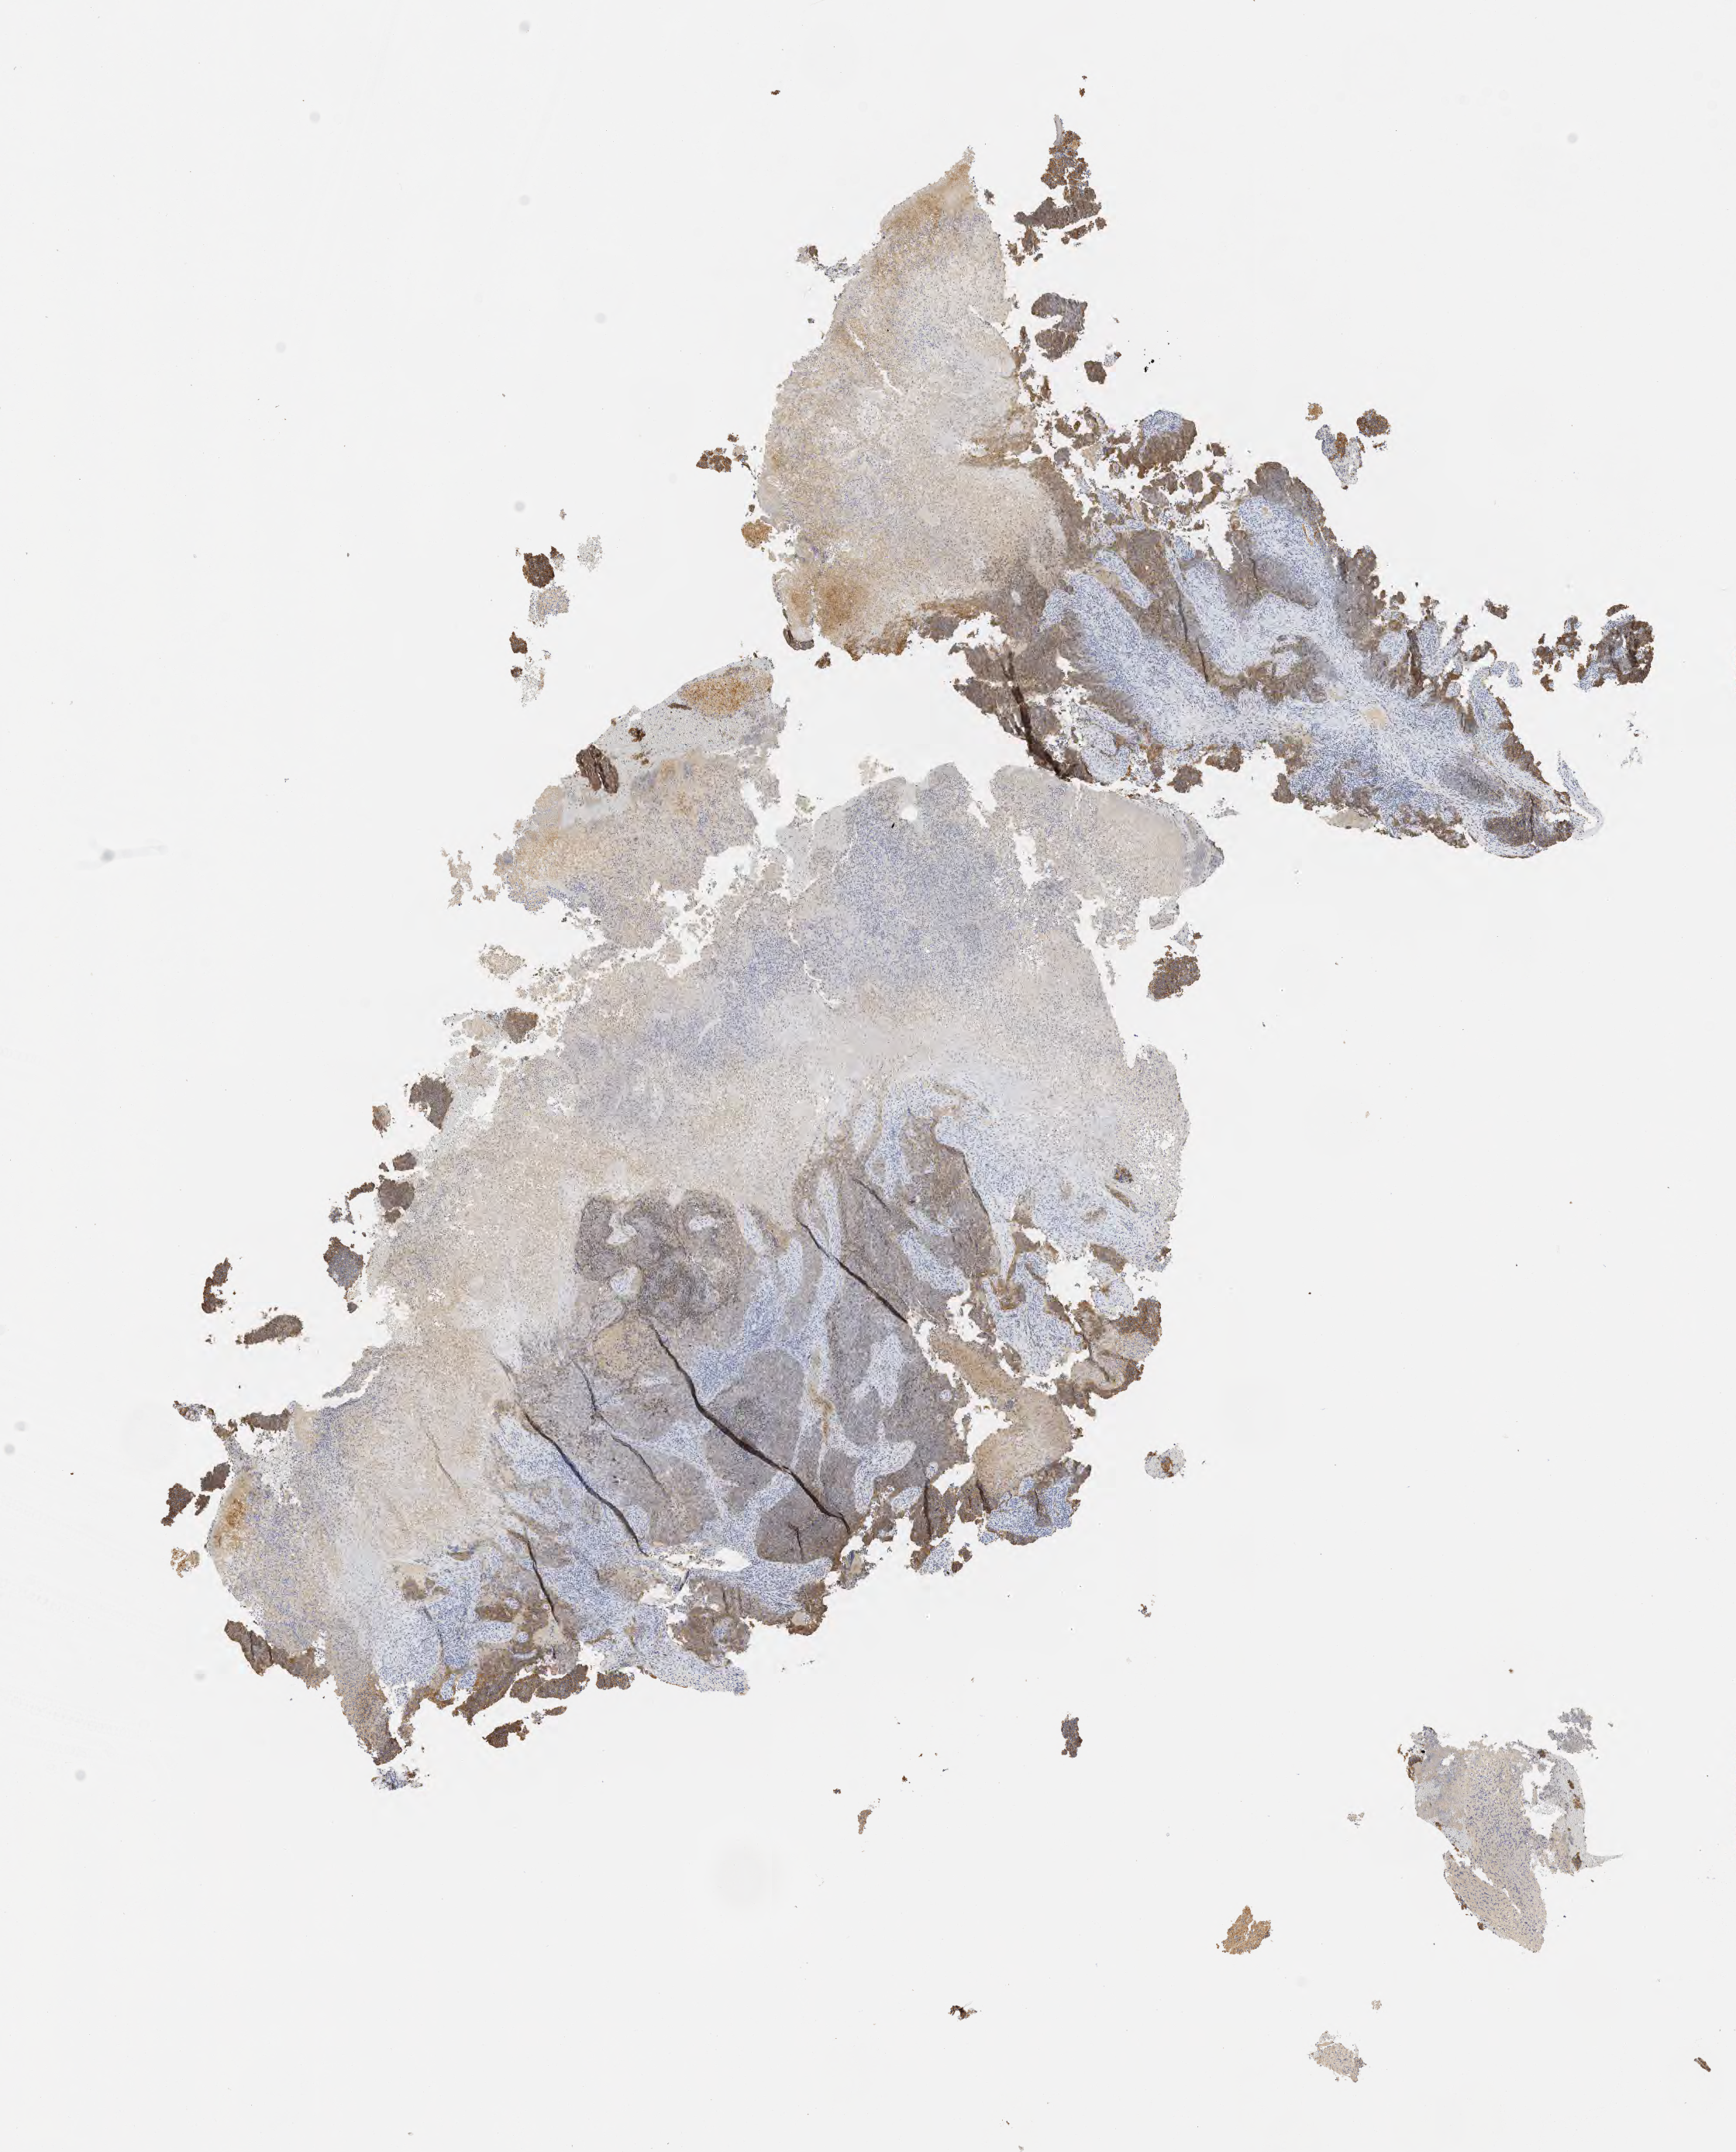
Immunohistochemistry (IHC) whole-slide image stained for Ber-EP4, whole scanned area (about 9.1 x 11.2 mm) shown as a low-resolution overview. Specimen: tumor tissue. Anatomic site: cervix. Patient: female, age 65 years.
- diagnosis: Squamous cell carcinoma, large cell, nonkeratinizing, NOS